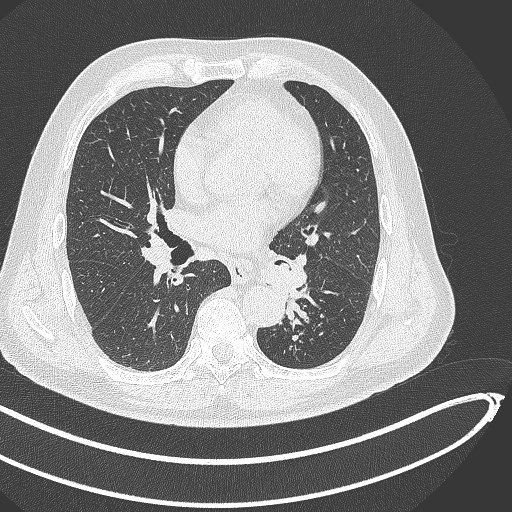
Chest CT, one axial slice. Position 241 of 468 along the scan axis. 120 kVp. Lung window (W 1500 / L -600 HU). 512 × 512 image matrix. Patient: male, 64 years. From the clinical record (not read from this slice): clinical TNM (as recorded): T1c N0 M0.
Outlined on this slice (rectangle marked by the reading radiologist):
- lung tumour (recorded histology: squamous cell carcinoma): bounding box (x1, y1, x2, y2) in pixels: (262, 253, 304, 325)